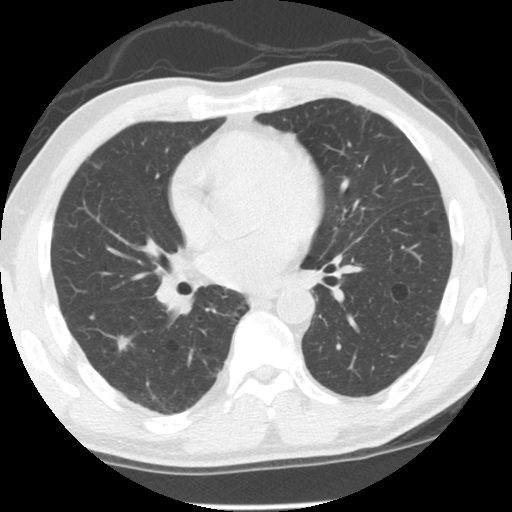
Low-dose screening chest CT, axial slice; baseline screening round; lung window (W 1500 / L -600 HU); standard (soft-tissue) reconstruction kernel (STANDARD); slice 56 of 125 in the series. Male participant, aged 60 years at enrolment. Former smoker at enrolment.
Expert reader's lesion annotation, box from (x=93, y=323) to (x=145, y=368) px. Screening reader's record for this exam (one nodule recorded; not confirmed to be the boxed lesion): non-calcified nodule or mass ≥4 mm, right lower lobe, 9 × 7 mm, spiculated (stellate) margins. Lung cancer was diagnosed 534 days after this screen (after the second annual screen): adenocarcinoma, NOS, right lower lobe, stage IA (AJCC 6th edition), 18 mm at pathology.